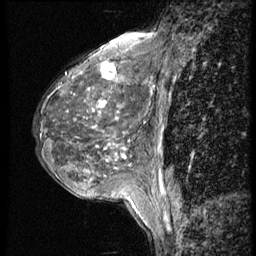
Breast MRI (dynamic contrast-enhanced), one sagittal slice. Position 19 of 56 along the scan axis. 4 images stored at this slice position (order not interpretable as contrast timing). 1.5 T. TE 4.2 ms, TR 9 ms. 256 × 256 image matrix, field of view 180 × 180 mm. Patient: female, 50 years. Case-level facts recorded for this patient, not image findings: setting: breast cancer imaged before/during neoadjuvant chemotherapy; receptor status: triple-negative.
Annotated regions visible in this slice (semi-automatically segmented with operator editing):
- analysis volume of interest (the breast-tissue region the enhancement analysis was run in; not a lesion): bounding box [x1, y1, x2, y2] px = [32, 46, 148, 188]
- tumour enhancement mask (voxels above the 140 % enhancement threshold inside the analysis volume of interest): [100, 49, 126, 158]